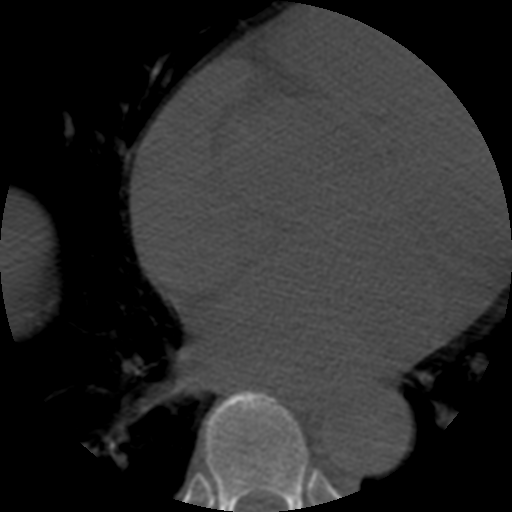
CT including the spine, one axial slice. Position 339 of 508 along the scan axis. Reconstruction kernel STANDARD. 120 kVp. Bone window (W 1800 / L 400 HU). 512 × 512 image matrix, field of view 160 × 160 mm. Patient age 57 years. Case-level facts recorded for this patient, not image findings: primary cancer: prostate.
Annotated regions visible in this slice (semi-automatically segmented with operator editing):
- T7 vertebra: bounding box (x1, y1, x2, y2) in pixels: (205, 392, 309, 512)